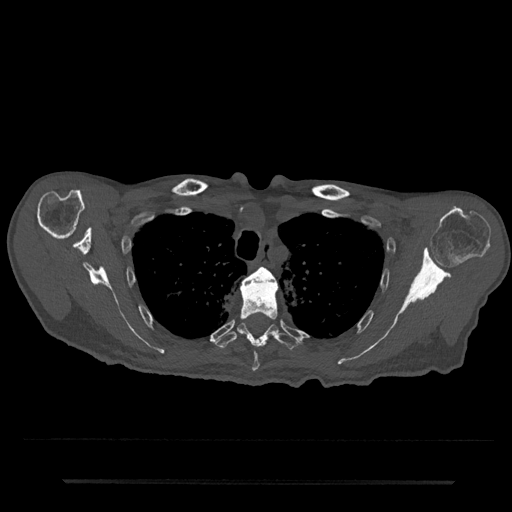
CT including the spine, one axial slice; position 607 of 797 along the scan axis; 120 kVp; bone window (W 1800 / L 400 HU); 0.5 mm slice thickness; 512 × 512 image matrix. Patient: male, 74 years. Case-level facts recorded for this patient, not image findings: primary cancer: prostate.
Annotated regions visible in this slice (semi-automatic segmentation, software-assisted and operator-edited):
- T3 vertebra: bounding box [x1, y1, x2, y2] px = [242, 267, 276, 284]
- T4 vertebra: [240, 276, 278, 372]
- T5 vertebra: [214, 323, 300, 350]